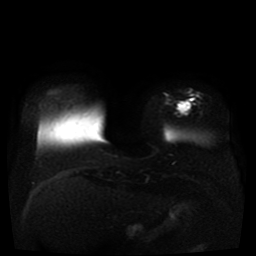
Breast MRI, one axial slice; slice 8 of 41 in the series (ordered by position); diffusion-weighted series; image 2 of 4 stored at this slice position (different b-values; order by instance number); 1.5 T; 5 mm slice thickness; 256 × 256 image matrix, field of view 330 × 330 mm. Female patient.
Structures marked on this image (outlined manually by an expert reader):
- tumour on diffusion-weighted imaging: bounding box [x1, y1, x2, y2] px = [178, 102, 190, 113]